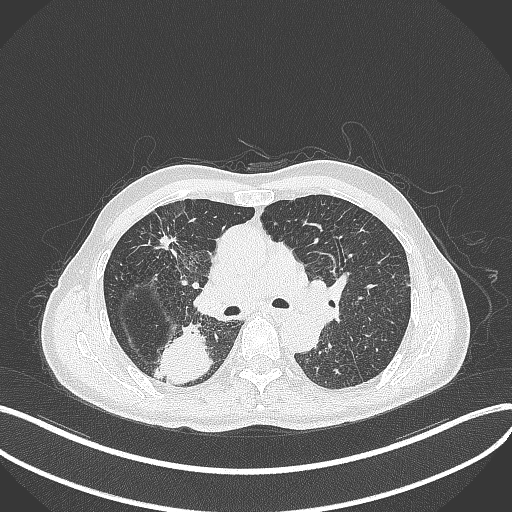
Chest CT, one axial slice; slice 276 of 428 in the series (ordered by position); 120 kVp; lung window (W 1500 / L -600 HU); 1 mm slice thickness; 512 × 512 image matrix. Patient: male, 79 years. From the clinical record (not read from this slice): clinical TNM (as recorded): T3 N0 M0.
Annotated regions visible in this slice (bounding box drawn by a radiologist):
- lung tumour (recorded histology: adenocarcinoma): bounding box (x1, y1, x2, y2) in pixels: (157, 324, 211, 385)